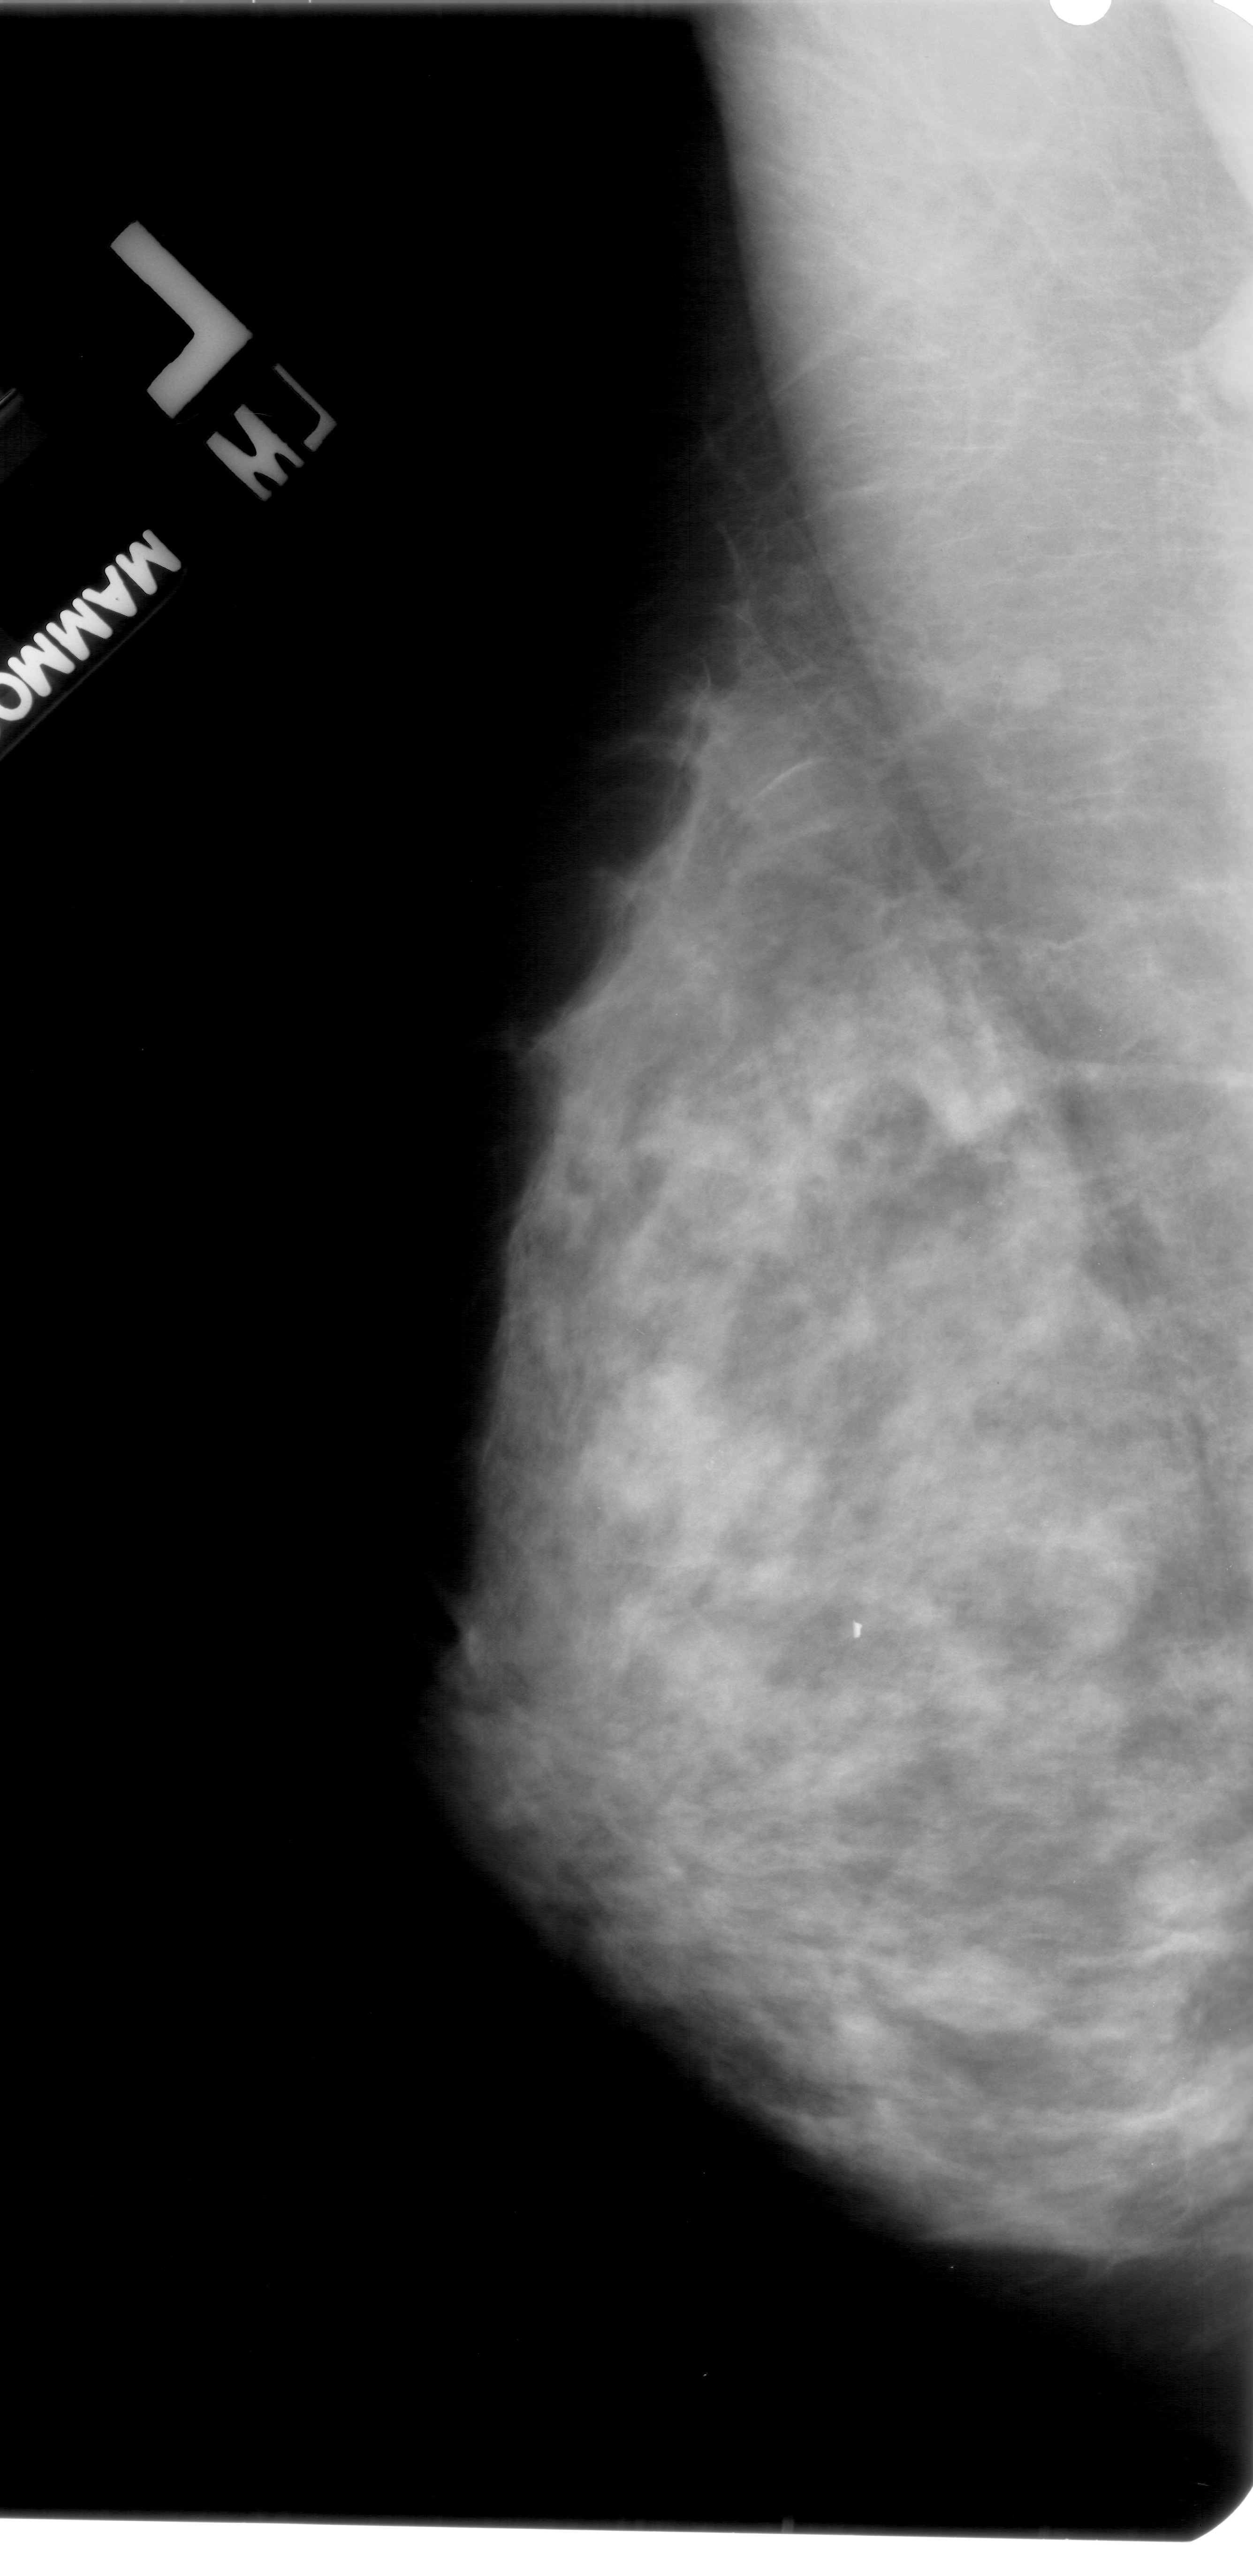
Digitized screen-film mammogram; left breast; MLO view; breast composition: extremely dense (BI-RADS density category 4 of 4).
Marked findings (only marked abnormalities are described; nothing is implied about the rest of the image): calcifications, morphology pleomorphic, distribution clustered; BI-RADS assessment category 4; subtlety rating 1 on a 1 (subtle) to 5 (obvious) scale; pathology result (as recorded, not read from the image): benign.